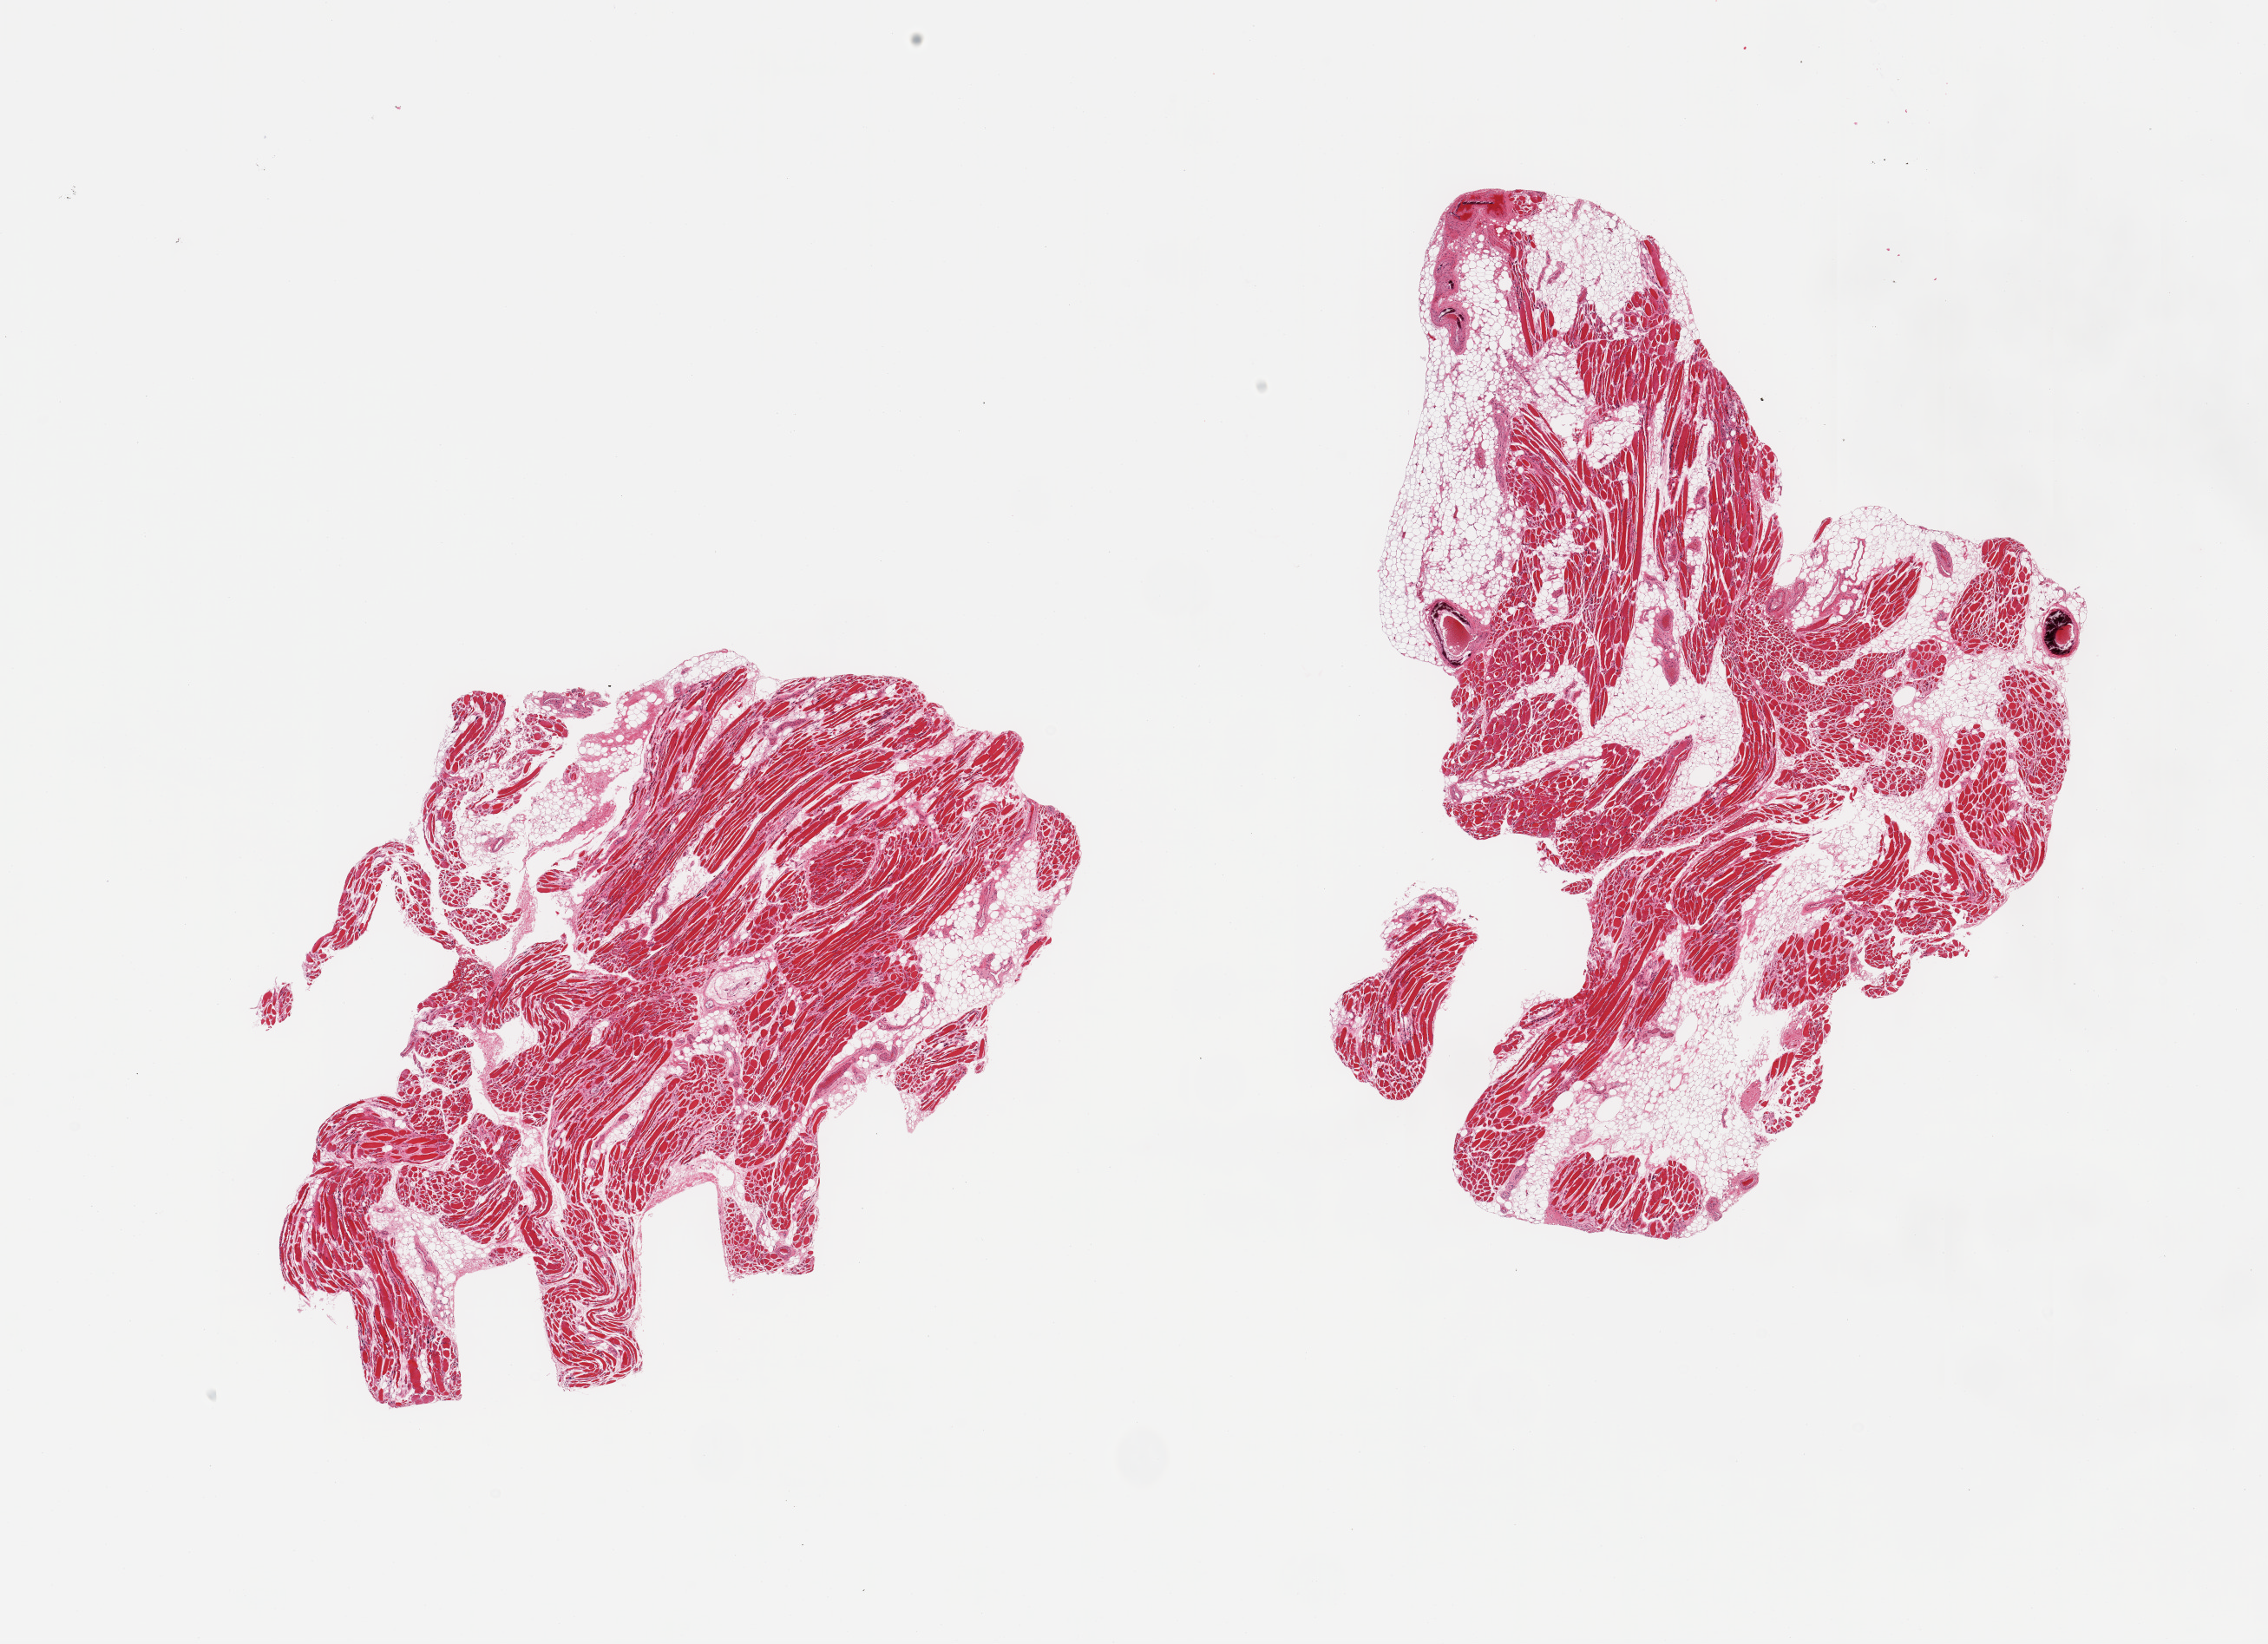
Hematoxylin and eosin (H&E) whole-slide image, shown as a low-resolution overview of the whole scanned area (about 20.7 x 15.0 mm); PAXgene-fixed paraffin-embedded (PFPE) section; target tissue: skeletal muscle; tissue donor sample. Female donor.
- pathologist's review note for this sample: 2 pieces, ~30% interstititial fat; moderate myocytic atrophy